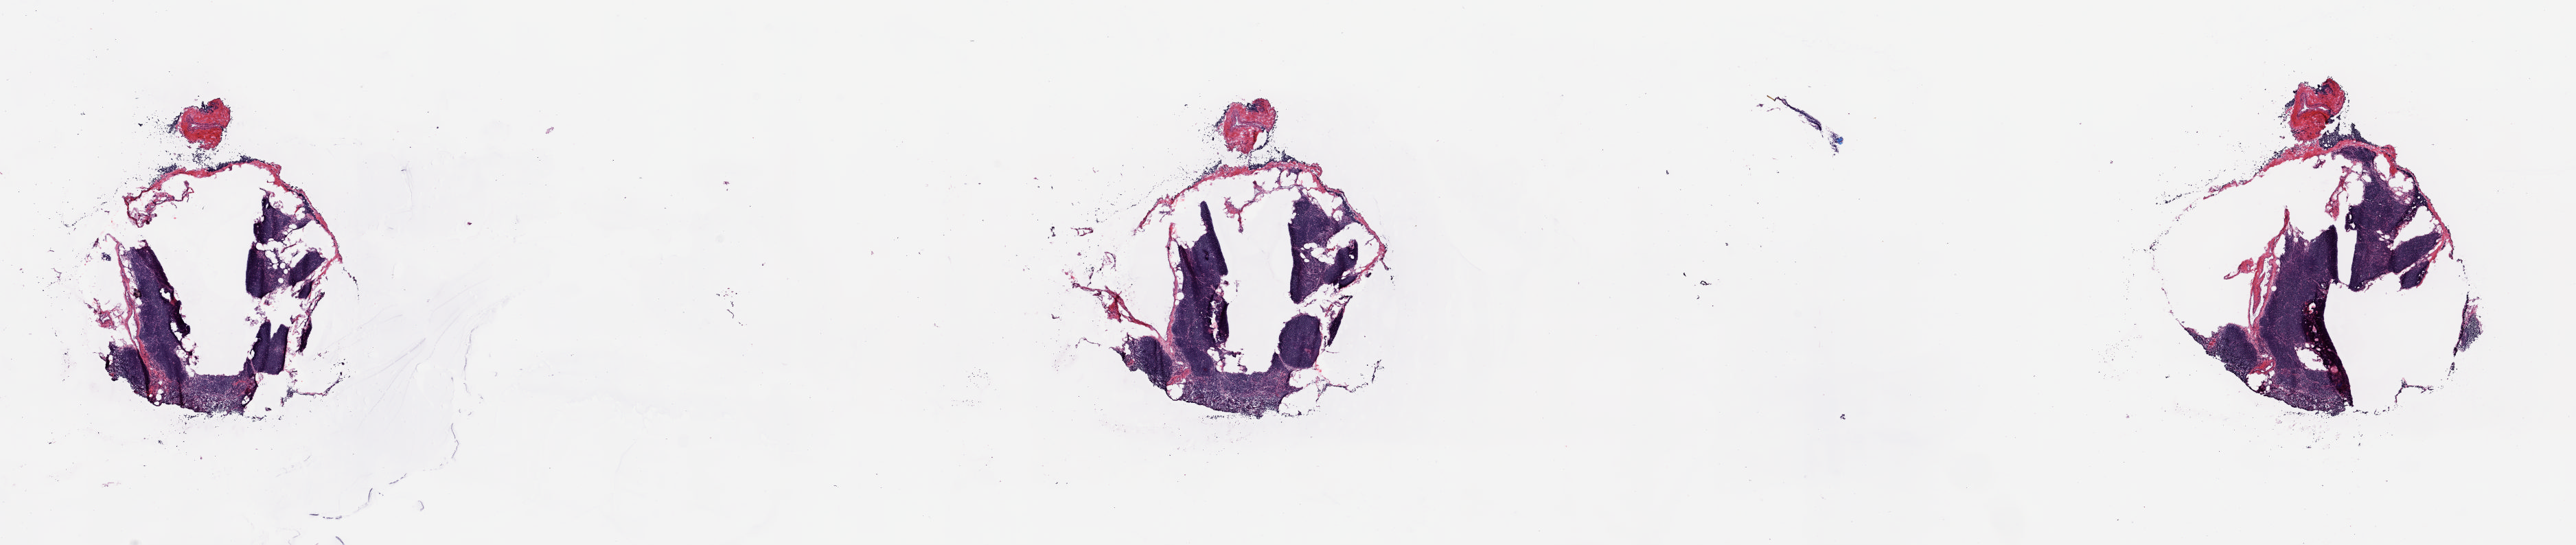
H&E whole-slide image, low-resolution overview of the scanned area, about 29.8 x 6.3 mm (slide scanned at 20x). Frozen section from the top of the tissue portion. Solid tissue normal (non-tumour tissue) sample from the thymus. Female patient; age at initial diagnosis 46 years. Slide review estimates, as recorded: tumour cells 0%, tumour nuclei 0%, normal cells 100%, stromal cells 0%, necrosis 0%. Inflammatory infiltration, as recorded: lymphocyte infiltration 0%, monocyte infiltration 0%, neutrophil infiltration 0%.
This section: solid tissue normal sample (biorepository sample class). Patient diagnosis: Thymoma, type B1, malignant.